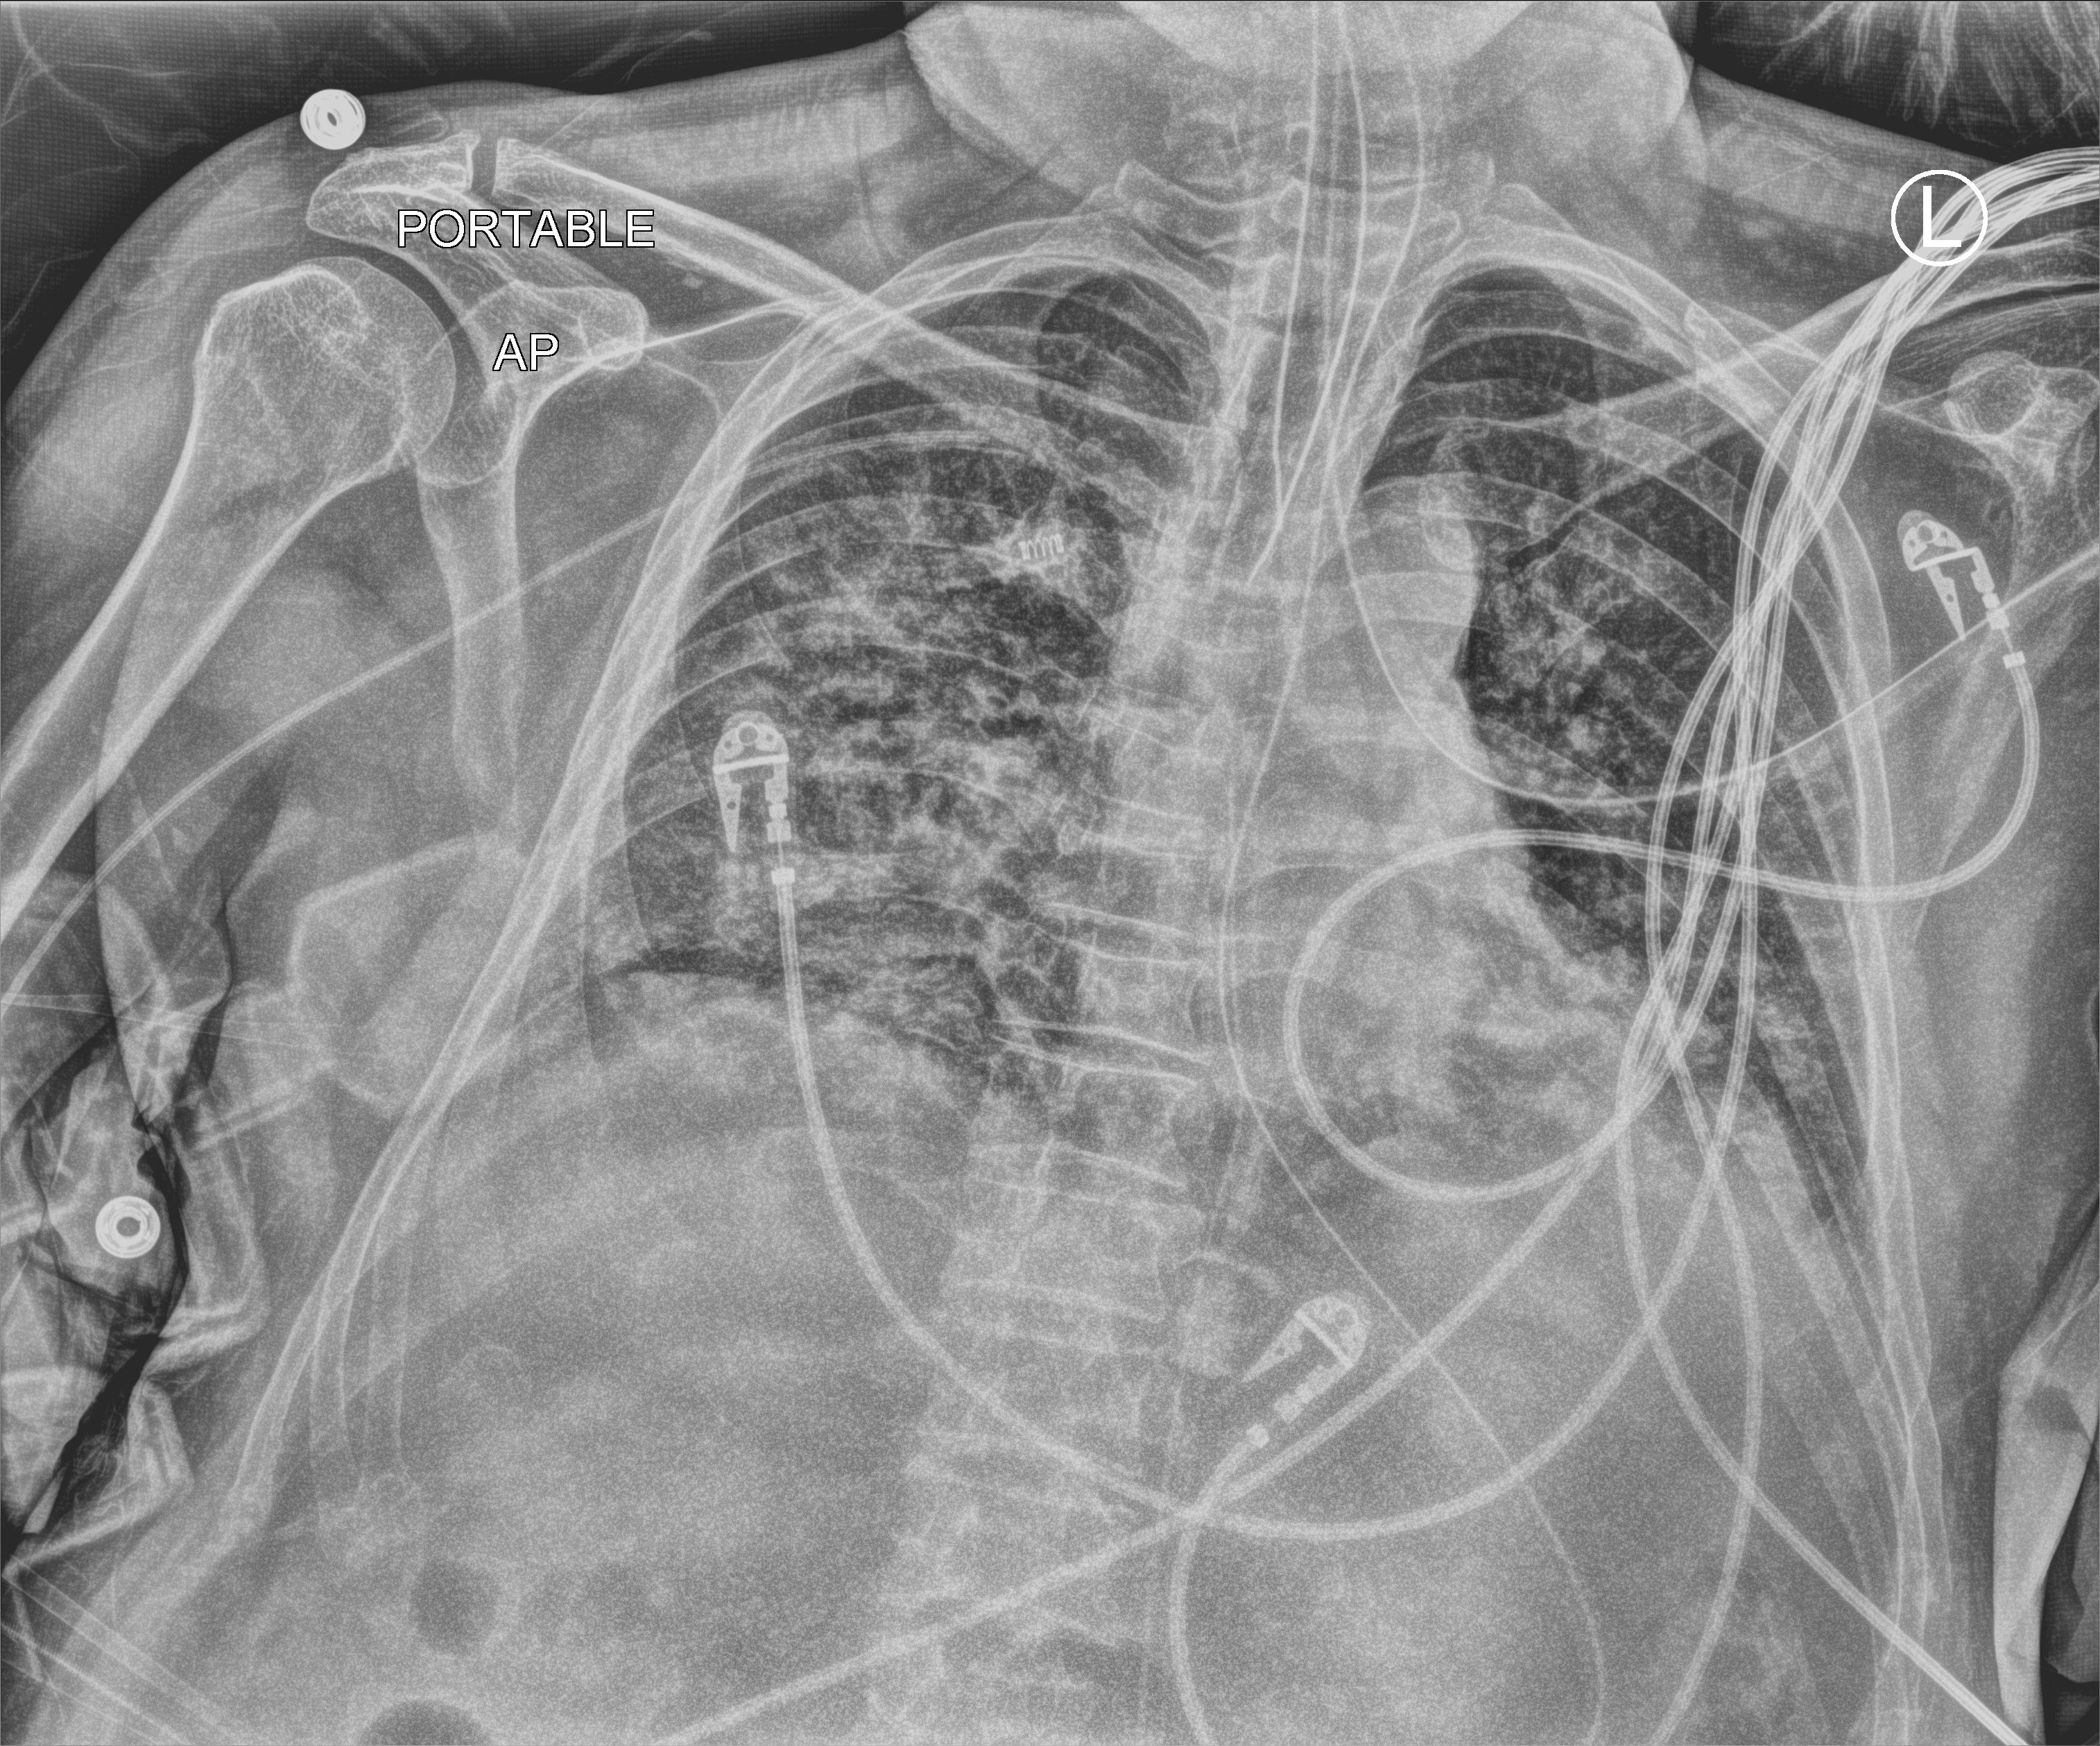
Chest X-ray (portable), anteroposterior (AP) projection. Patient hospitalised with COVID-19; male, aged 60–74 years.
From the hospital-stay record, not from the radiograph (when in the stay this image was taken is not recorded): smoking status (admission record): never; admitted to intensive care during this hospital stay: yes.